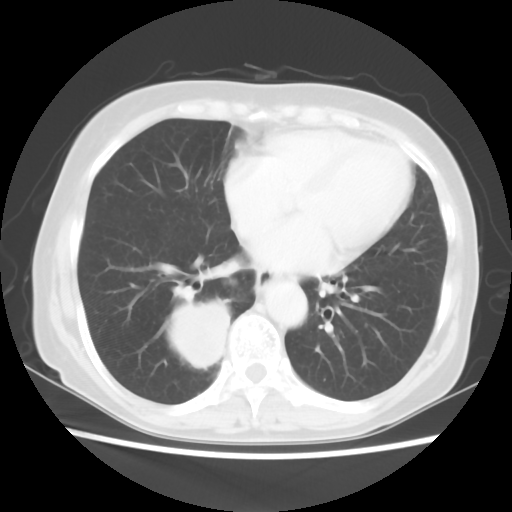
Chest CT, one axial slice; slice 21 of 56 in the series (ordered by position); reconstruction kernel STANDARD; 120 kVp; lung window (W 1500 / L -600 HU); 5 mm slice thickness; 512 × 512 image matrix, field of view 332 × 332 mm. Patient: female, 66 years. Case-level facts recorded for this patient, not image findings: clinical TNM (as recorded): T2 N3 M0; histopathological grade: G3.
Structures marked on this image (bounding box drawn by a radiologist):
- lung tumour (recorded histology: small cell carcinoma): bounding box [x1, y1, x2, y2] px = [163, 291, 231, 372]